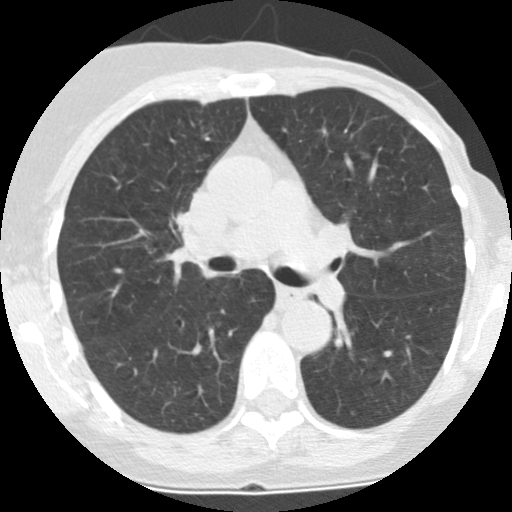
Chest CT (low-dose screening protocol), one axial image; first (baseline) screen; lung window (W 1500 / L -600 HU); 2.5 mm slice thickness; 120 kVp; slice 95 of 225 in the series; 512 × 512 image matrix, field of view 280 × 280 mm. Female participant, aged 66 years at enrolment. Former smoker at enrolment.
Expert-annotated lung lesion, box from (x=357, y=145) to (x=373, y=166) px. No non-calcified nodule or mass ≥4 mm was recorded by the screening reader at this exam. Official screen result: negative screen, minor abnormalities not suspicious for lung cancer. Lung cancer was diagnosed 583 days after this screen (after the second annual screen): adenocarcinoma, NOS, left lower lobe, poorly differentiated (G3), stage IA (AJCC 6th edition), 8 mm at pathology.